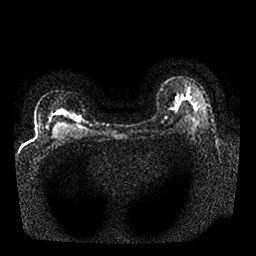
Breast MRI, one axial slice. Position 17 of 25 along the scan axis. Diffusion-weighted series; image 2 of 4 stored at this slice position (different b-values; order by instance number). 1.5 T. 4 mm slice thickness. 256 × 256 image matrix, field of view 340 × 340 mm. Female patient.
Outlined on this slice (manually delineated by an expert):
- tumour on diffusion-weighted imaging: box from (x=69, y=113) to (x=81, y=123) px